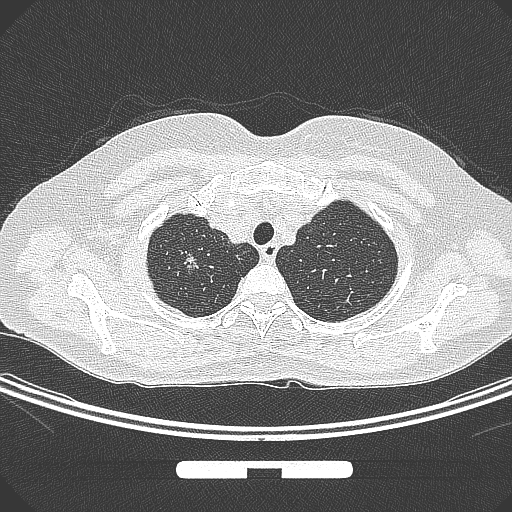
Chest CT, one axial slice. Slice 255 of 295 in the series (ordered by position). 120 kVp. Lung window (W 1500 / L -600 HU). 1 mm slice thickness. 512 × 512 image matrix. Female patient, age 58 years. From the clinical record (not read from this slice): clinical TNM (as recorded): T1b N0 M0; histopathological grade: G2-3.
Outlined on this slice (rectangle marked by the reading radiologist):
- lung tumour (recorded histology: adenocarcinoma): bounding box <178,242,204,283> (left, top, right, bottom; pixels)